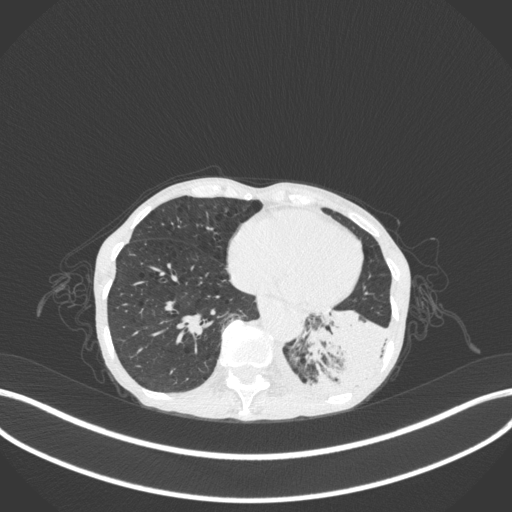
Chest CT, one axial slice; slice 65 of 347 in the series (ordered by position); reconstruction kernel B31f; lung window (W 1500 / L -600 HU); 1 mm slice thickness; 512 × 512 image matrix. Female patient, age 70 years. Case-level facts recorded for this patient, not image findings: clinical TNM (as recorded): T3 N0 M0.
Annotated regions visible in this slice (rectangle marked by the reading radiologist):
- lung tumour (recorded histology: small cell carcinoma): box from (x=303, y=303) to (x=394, y=407) px